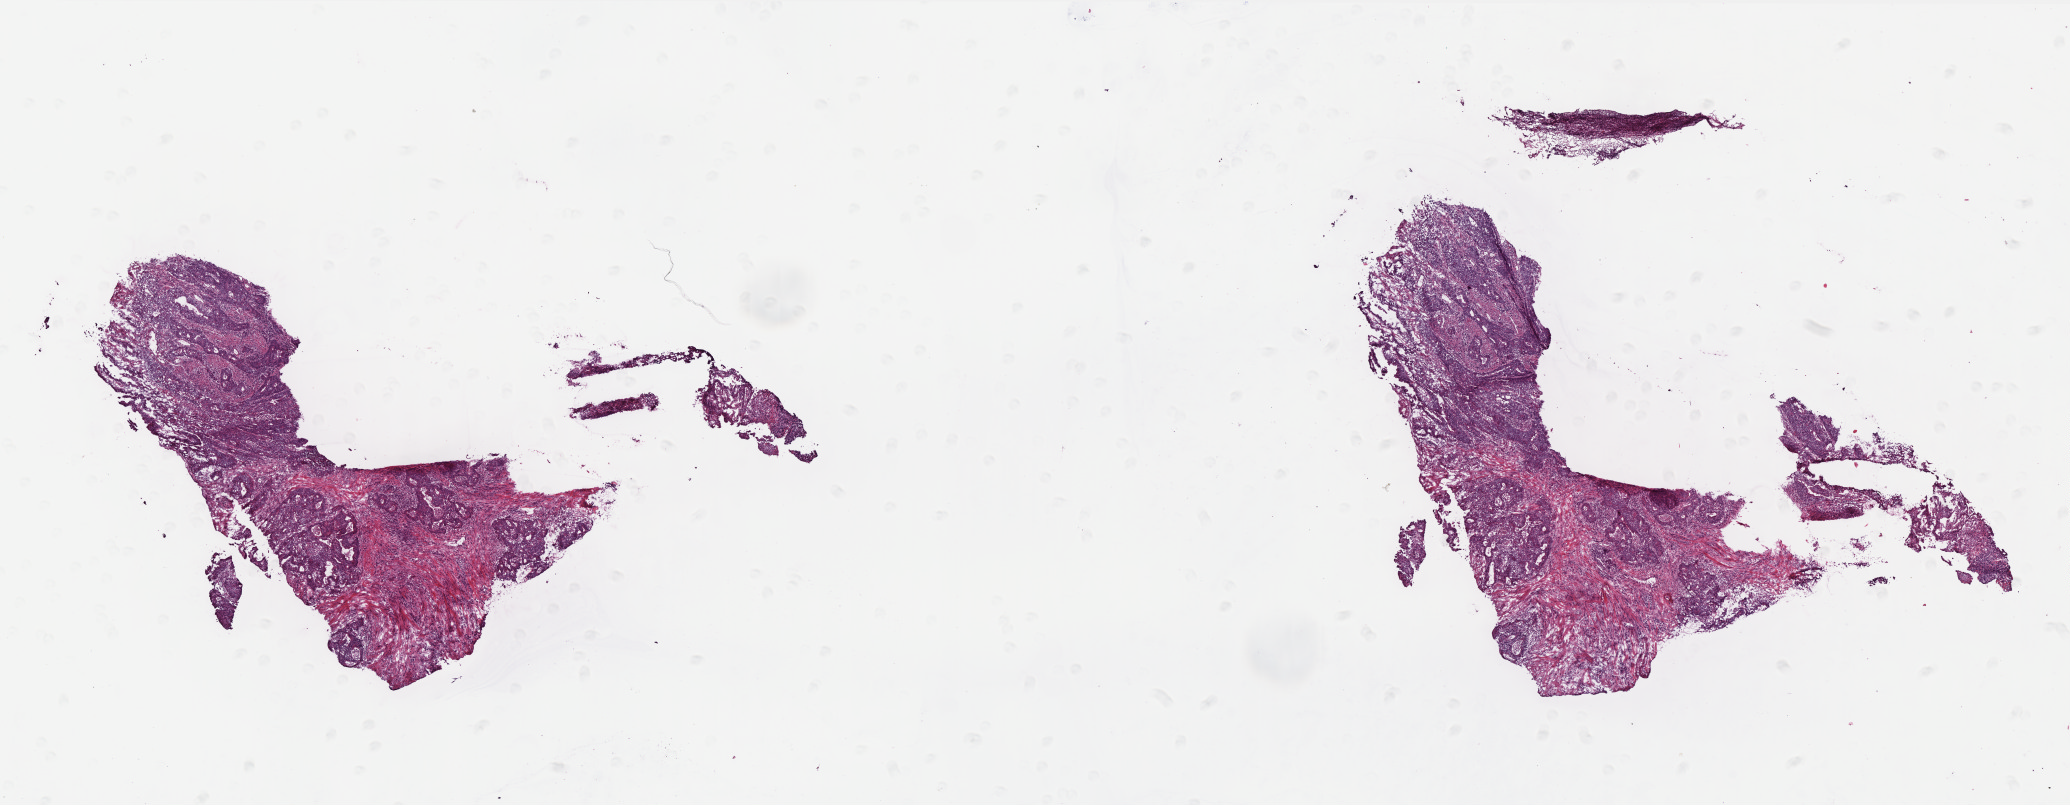
Digitized H&E tissue section (whole slide) — shown as a low-resolution overview of the whole scanned area (about 16.6 x 6.5 mm); frozen section; colon, primary tumour sample. Male patient; age at initial diagnosis 70 years. Pathologist review of this section (percent, as recorded): tumour cells 80%, tumour nuclei 80%, normal cells 0%, stromal cells 19%, necrosis 1%. Inflammatory infiltration, as recorded: lymphocyte infiltration 6%, monocyte infiltration 2%, neutrophil infiltration 6%.
Histologic diagnosis: Adenocarcinoma, NOS (ascending colon). Lymph nodes positive (case pathology): 0 of 28 examined. AJCC pathologic stage: I (6th edition).